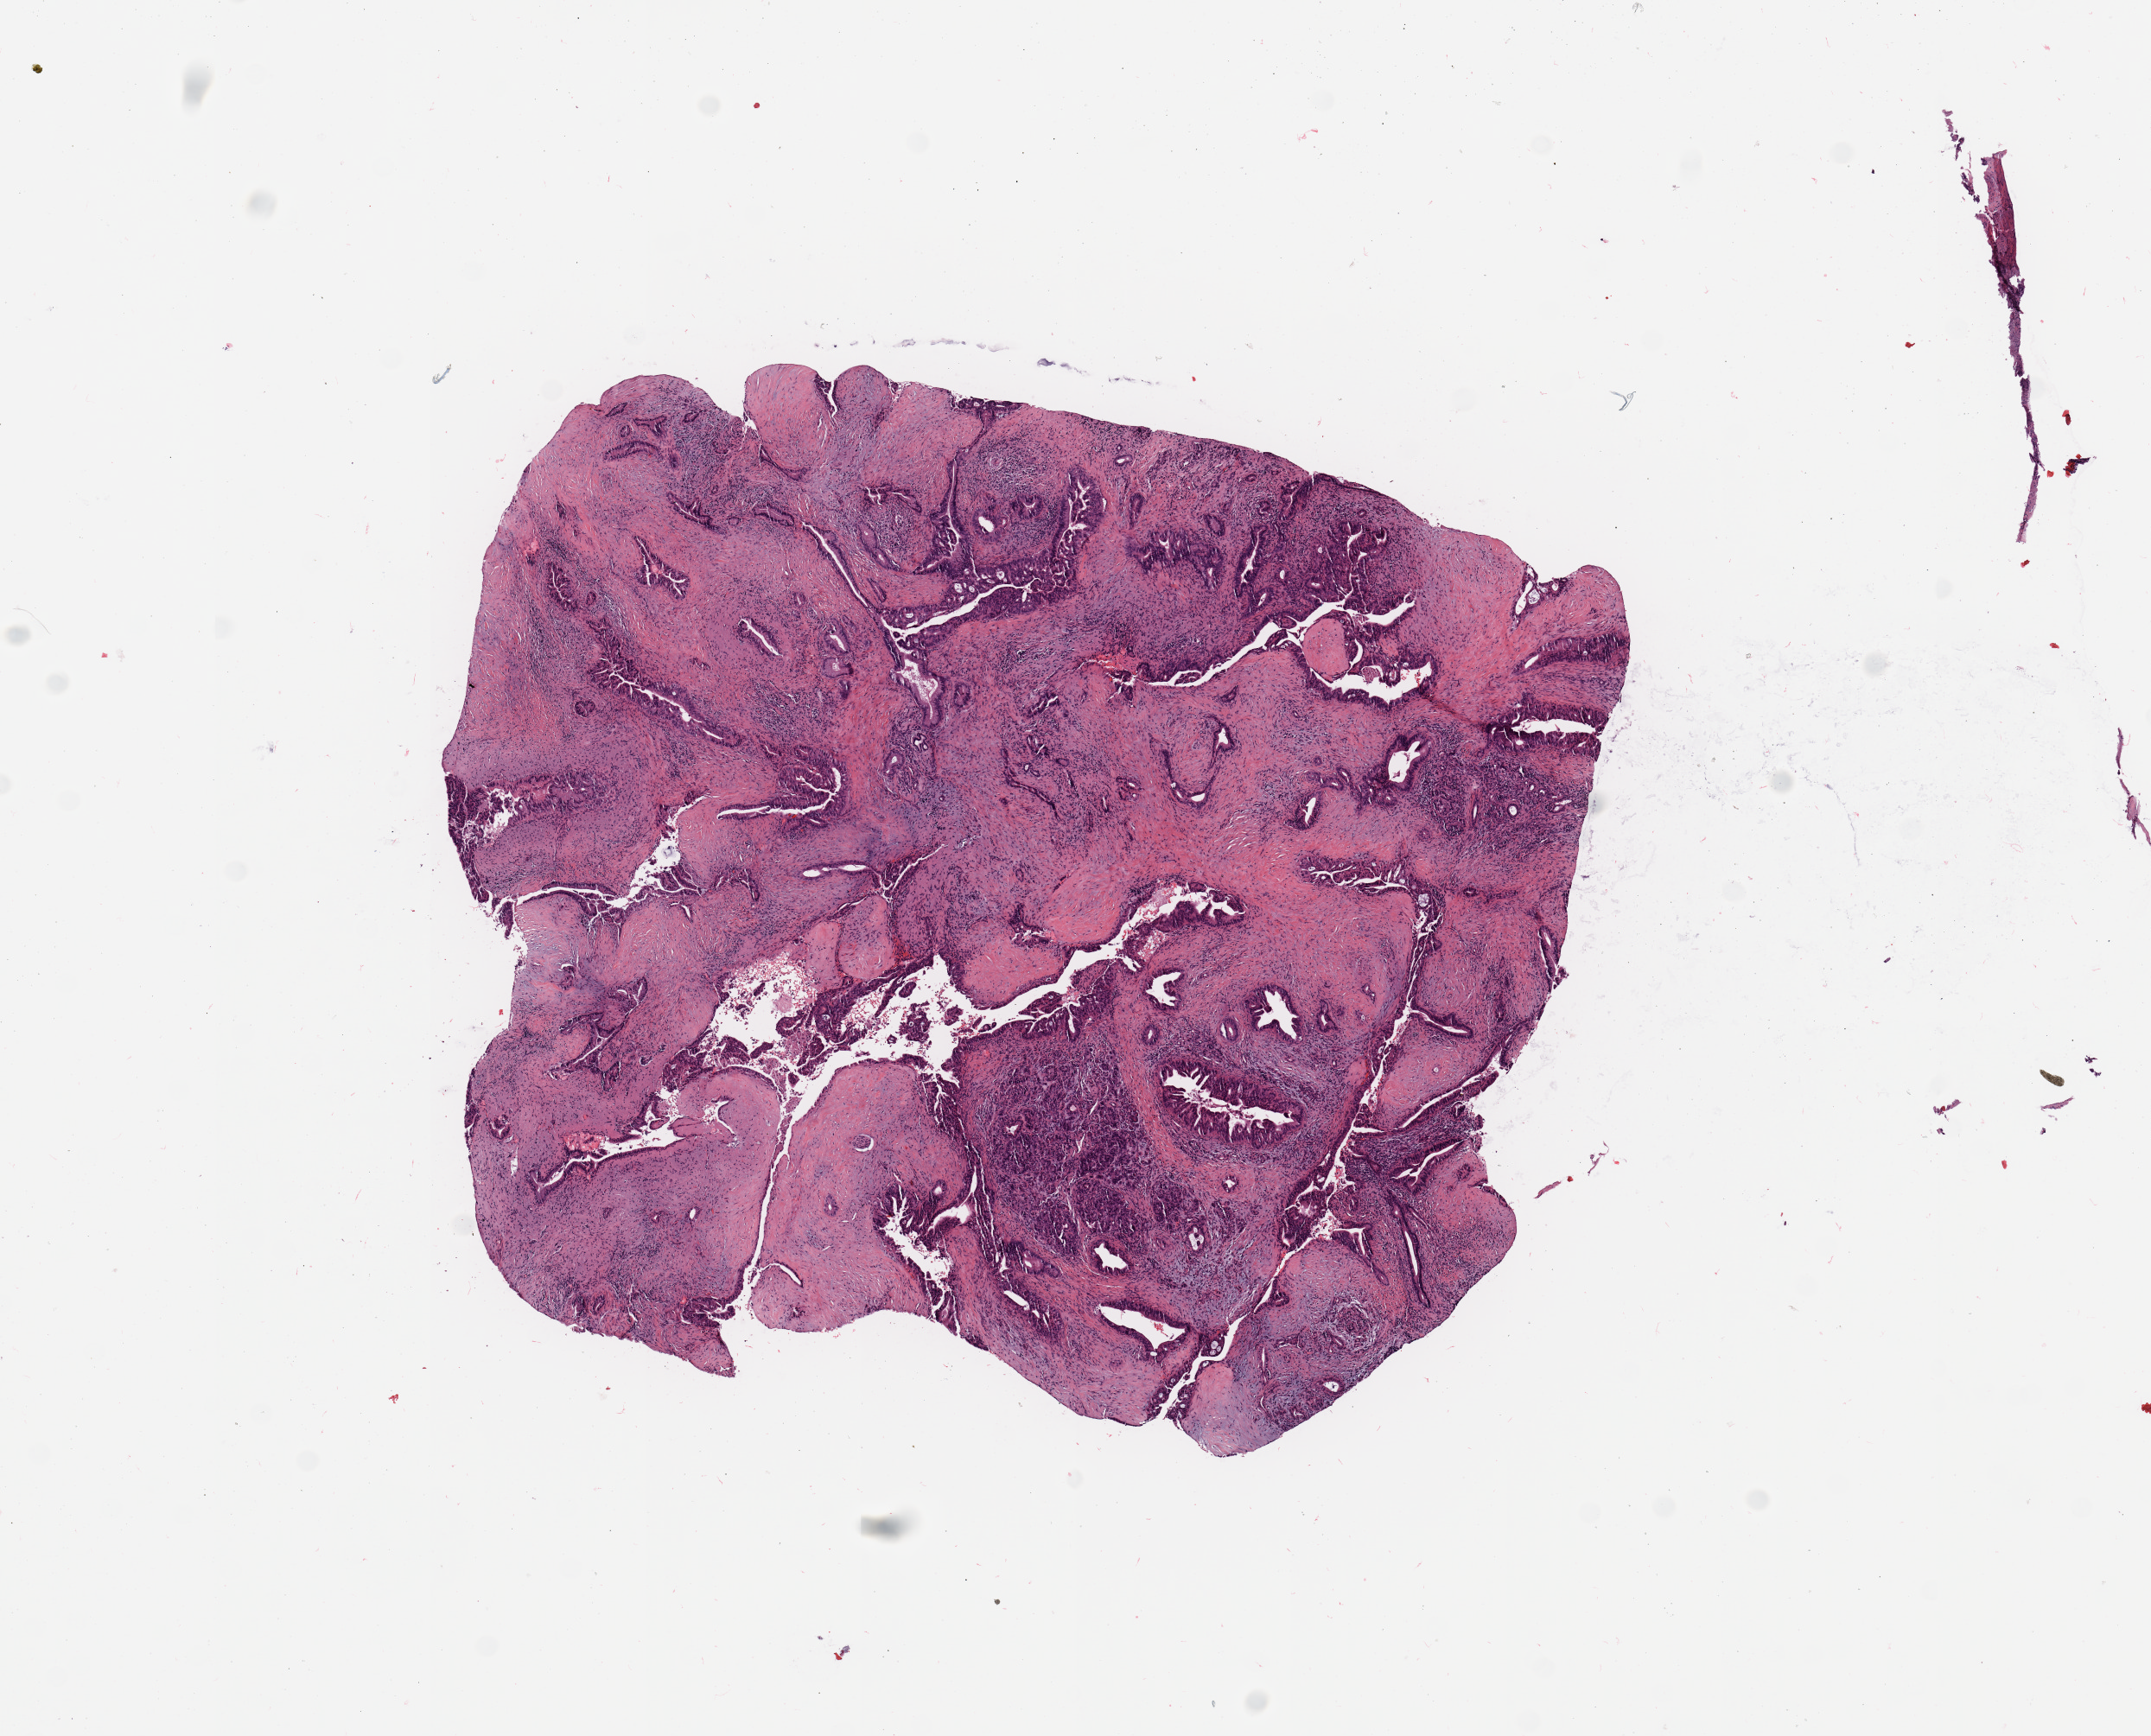
Digitized Hematoxylin and eosin (H&E) stained tissue section (whole slide) — whole scanned area (about 9.8 x 7.9 mm) shown as a low-resolution overview. Tumour tissue sample, pancreas. Patient: male, age 63 years. Histologic grade: G2 (moderately differentiated).
AJCC pathologic stage: IB. Primary tumour site (as recorded): head. Diagnosis: Infiltrating duct carcinoma, NOS.